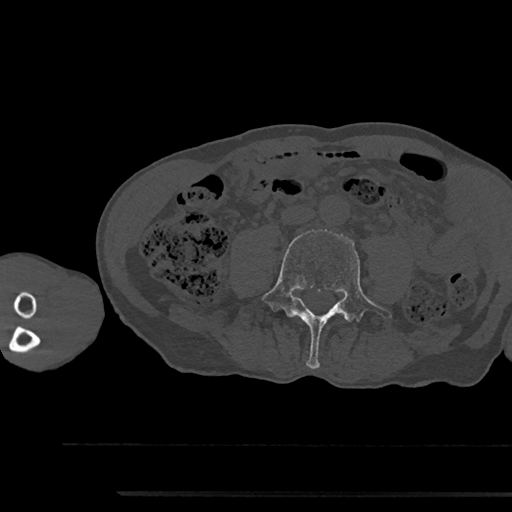
CT including the spine, one axial slice; position 420 of 797 along the scan axis; reconstruction kernel Br40s/3; 120 kVp; bone window (W 1800 / L 400 HU); 0.5 mm slice thickness; 512 × 512 image matrix, field of view 367 × 367 mm. Patient: male, 79 years. From the clinical record (not read from this slice): primary cancer: prostate.
Annotated regions visible in this slice (semi-automatically segmented with operator editing):
- L4 vertebra: bounding box [x1, y1, x2, y2] px = [261, 229, 392, 369]